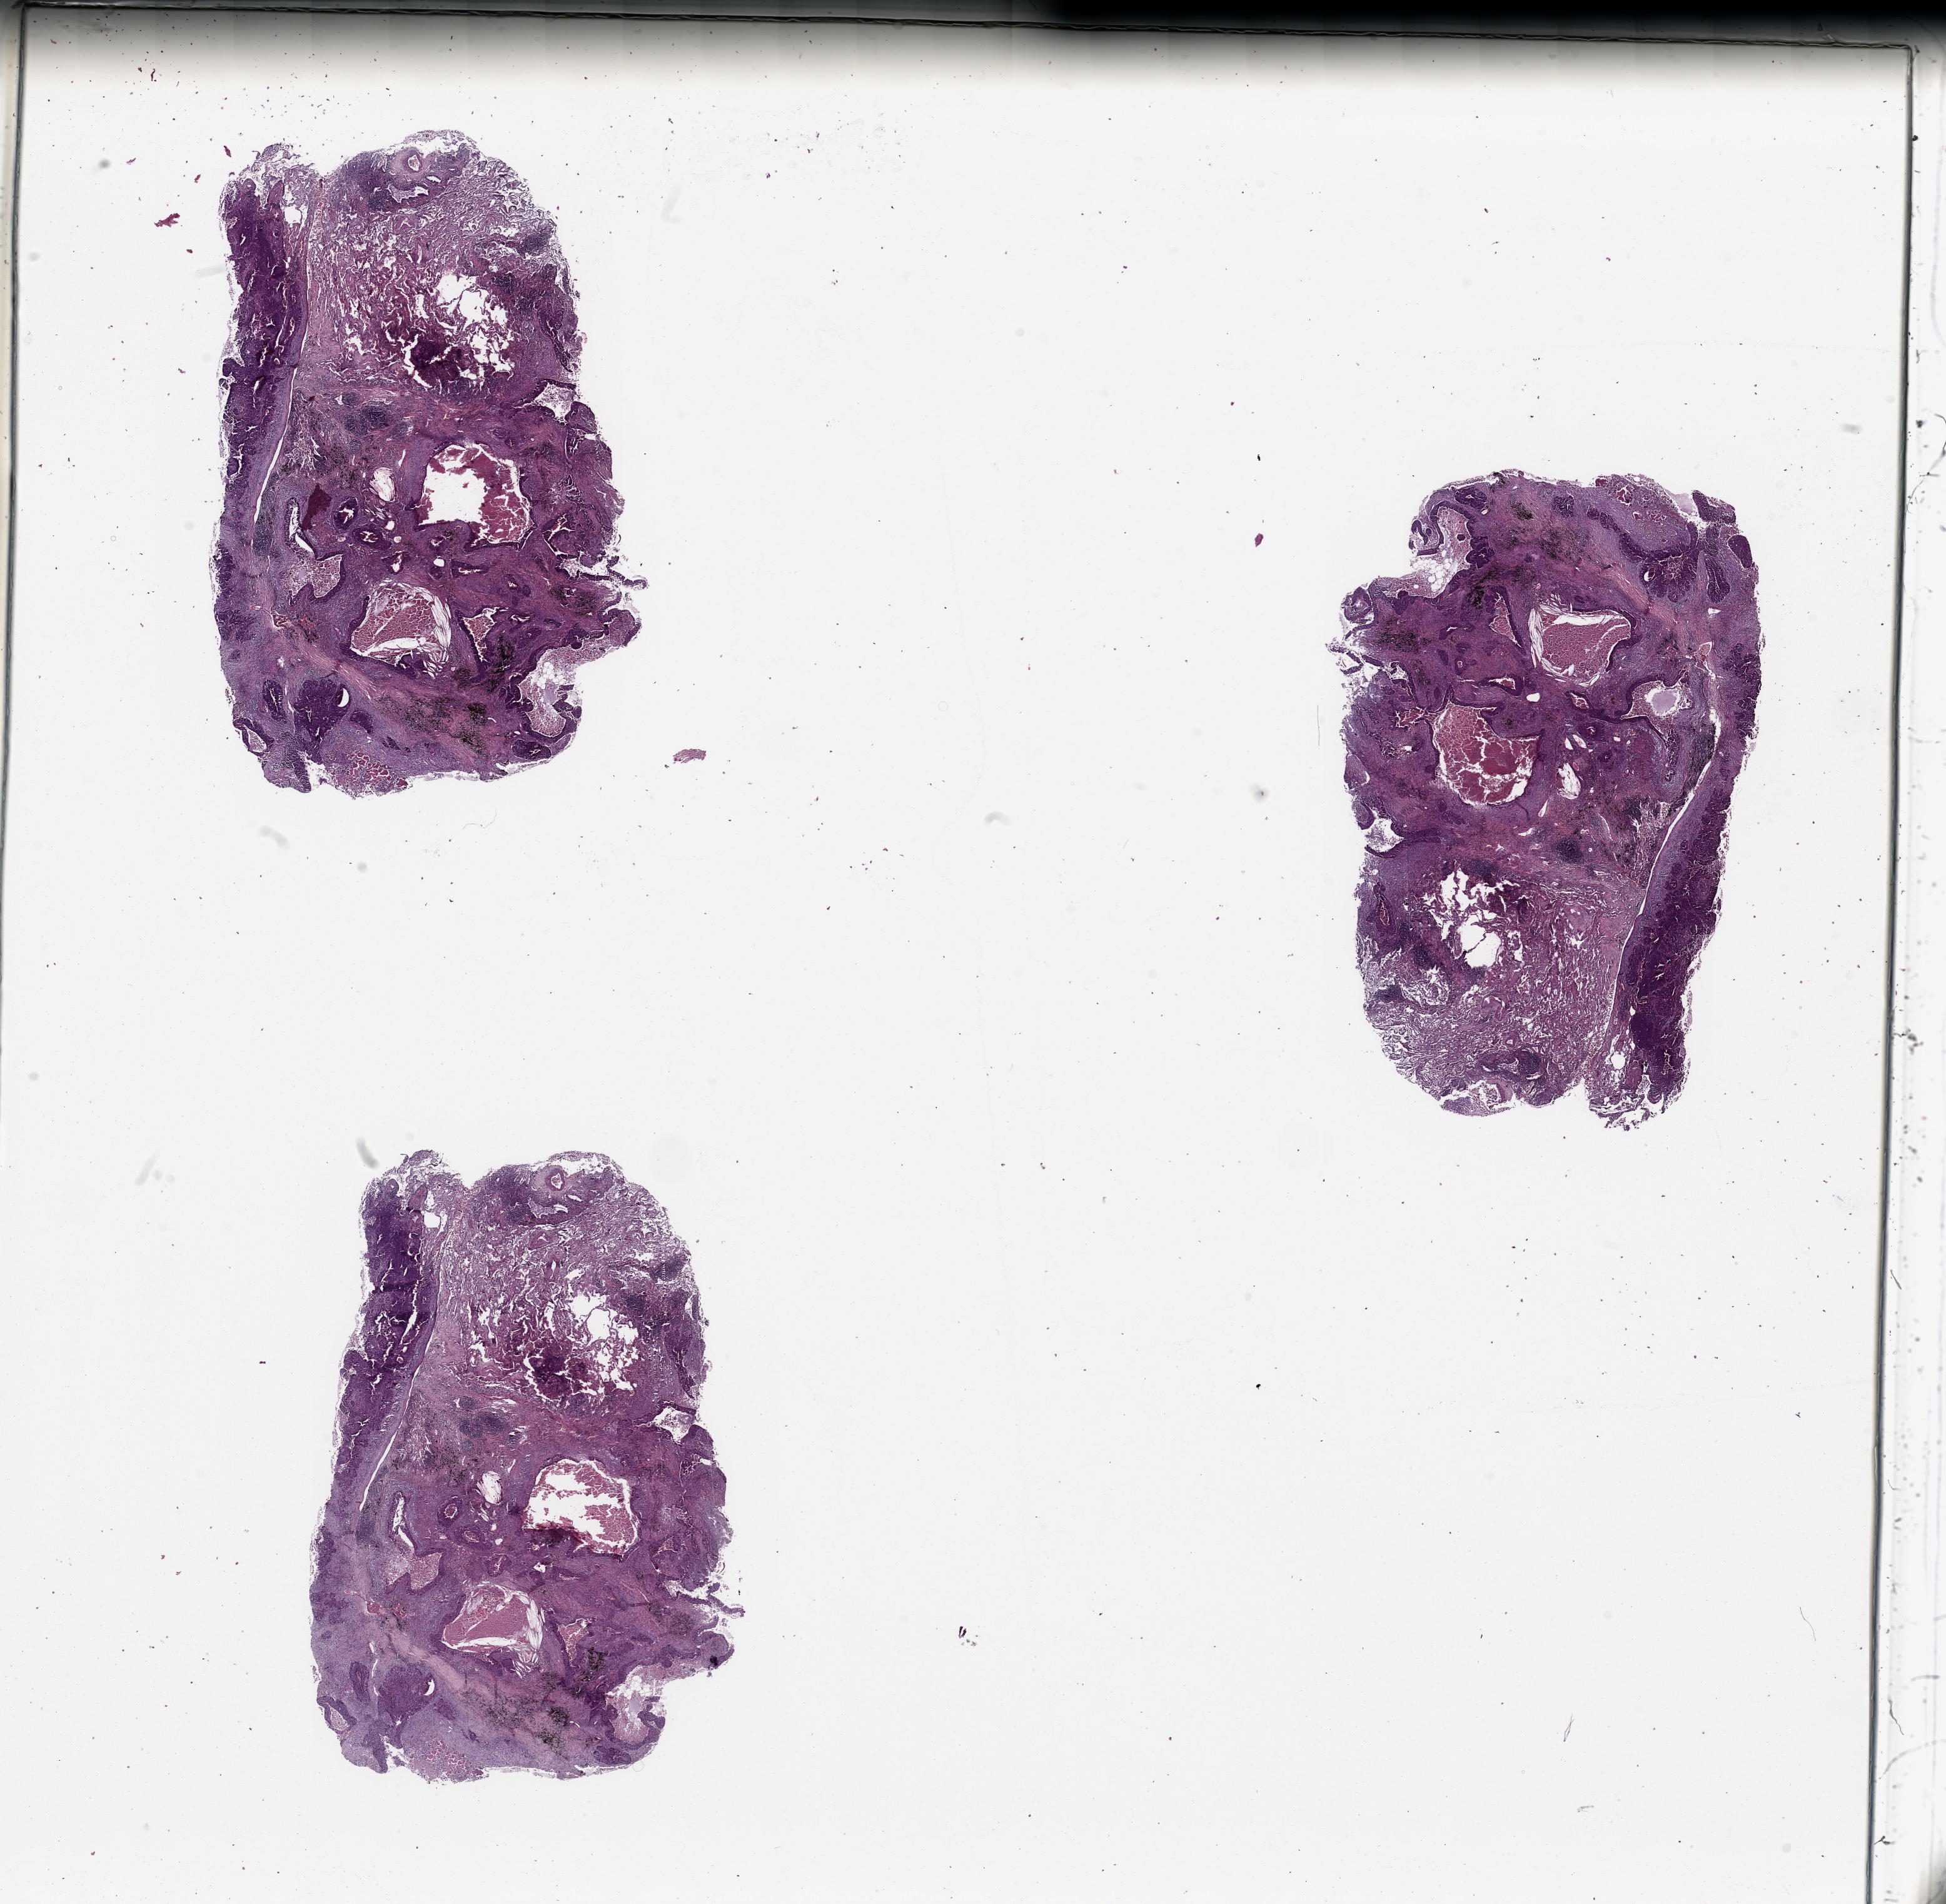
H&E whole-slide image — shown as a low-resolution overview of the whole scanned area (about 24.6 x 24.1 mm, from a 20x scan); lung, tumour tissue. Patient: male, age 76 years. Histologic grade: G2 (moderately differentiated).
- primary tumour site (as recorded): right middle lobe
- histologic diagnosis: Squamous cell carcinoma, NOS
- AJCC pathologic stage: IA